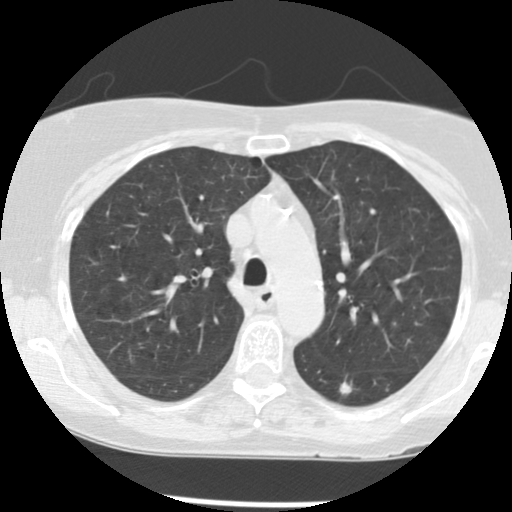
Chest CT (low-dose screening protocol), one axial image; second annual screen; lung window (W 1500 / L -600 HU); 2.5 mm slice thickness; 512 × 512 image matrix, field of view 292 × 292 mm. Female participant, aged 63 years at enrolment.
Lesion marked by an expert reader, bounding box <327,369,368,404> (left, top, right, bottom; pixels). The exam's reader record, not a measurement of the box and not confirmed to be the same lesion: non-calcified nodule or mass ≥4 mm, left lower lobe, 7 × 6 mm, poorly defined margins, soft tissue attenuation, pre-existing on the prior screen: yes; interval growth: yes. Official screen result: positive, other.